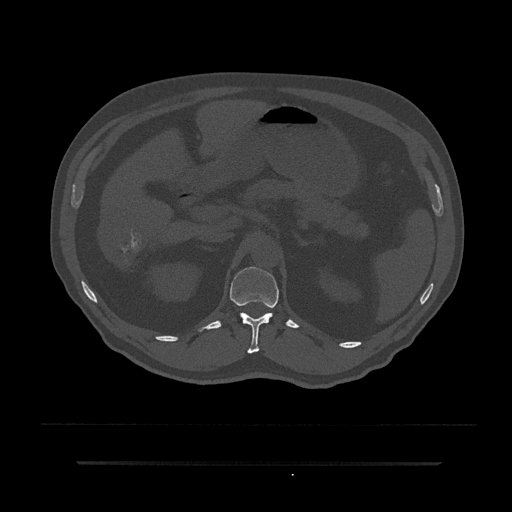
CT including the spine, one axial slice. Slice 201 of 797 in the series (ordered by position). Reconstruction kernel Br40s/3. Bone window (W 1800 / L 400 HU). 0.5 mm slice thickness. 512 × 512 image matrix. Patient: male, 59 years. From the clinical record (not read from this slice): primary cancer: bile ducts.
Structures marked on this image (semi-automatic segmentation, software-assisted and operator-edited):
- T12 vertebra: bounding box (x1, y1, x2, y2) in pixels: (230, 267, 279, 354)